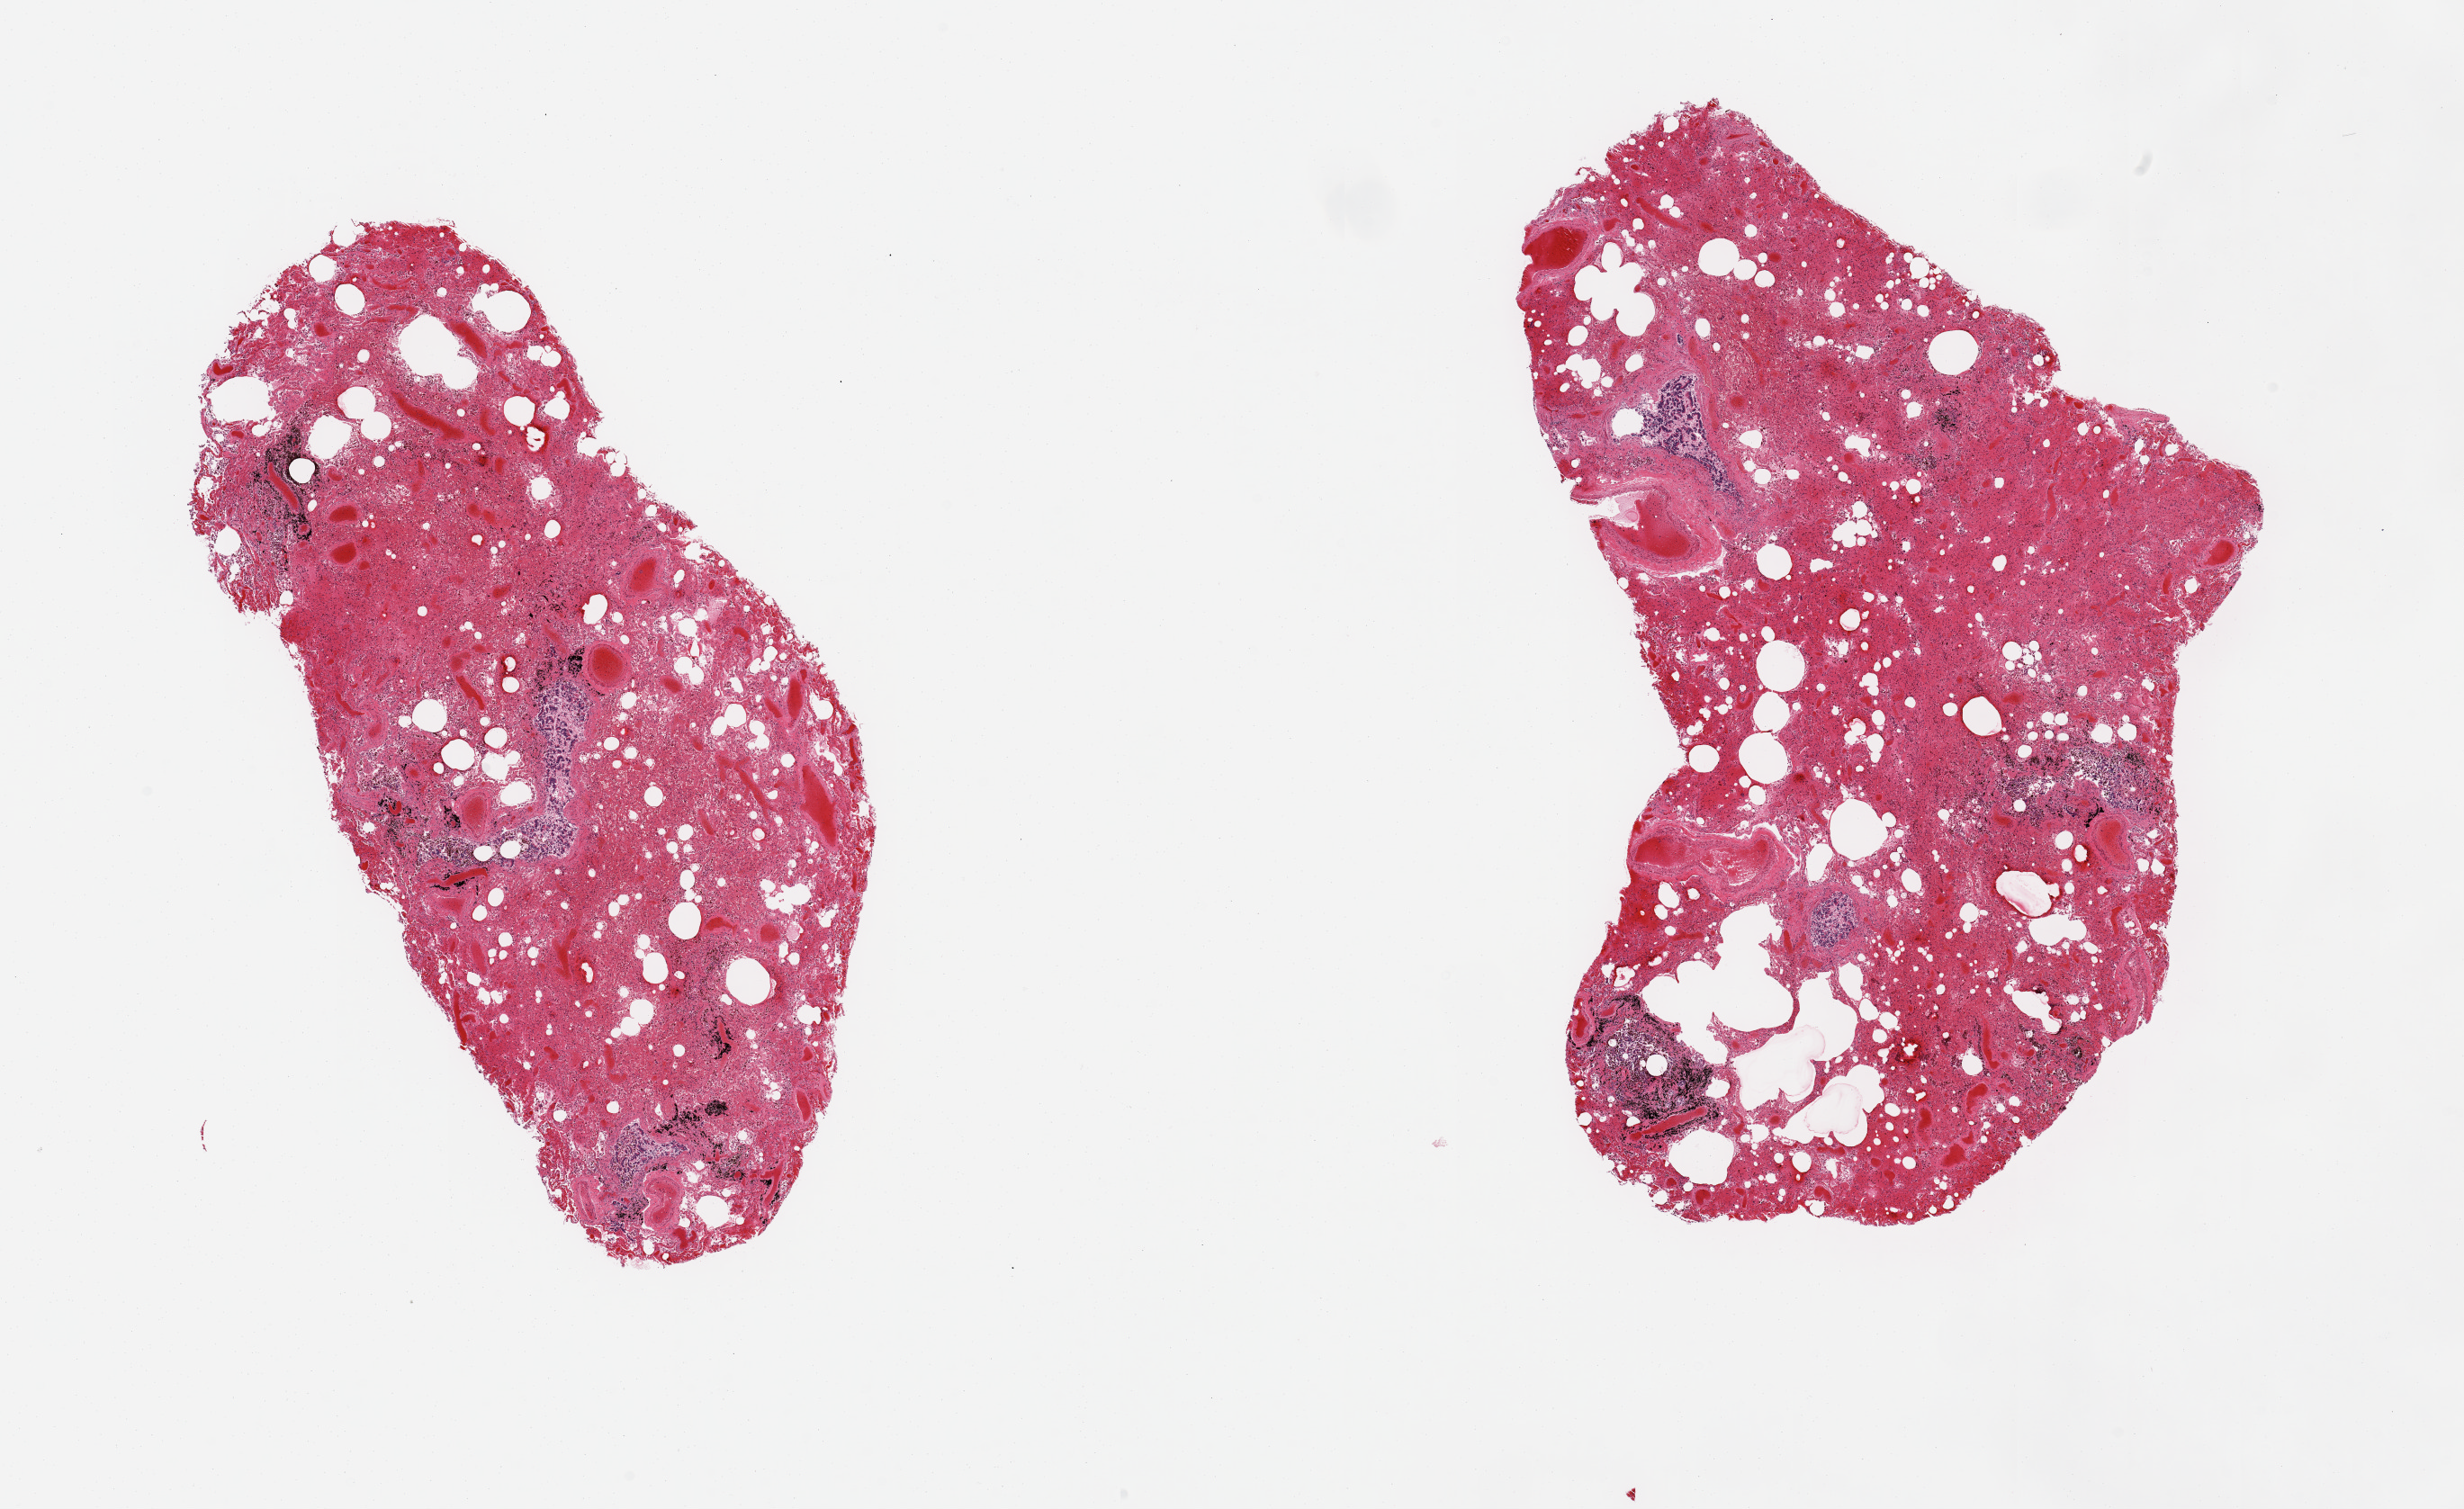
Whole-slide image, hematoxylin and eosin (H&E) stain — a low-resolution overview of the entire scanned area, about 21.7 x 13.3 mm (from a 20x scan). PAXgene-fixed paraffin-embedded (PFPE) section. Target tissue: lung. Donor tissue sample. Male donor.
Review note (as recorded): 2 pieces; marked congestion; sloughed bronchial epithelium.